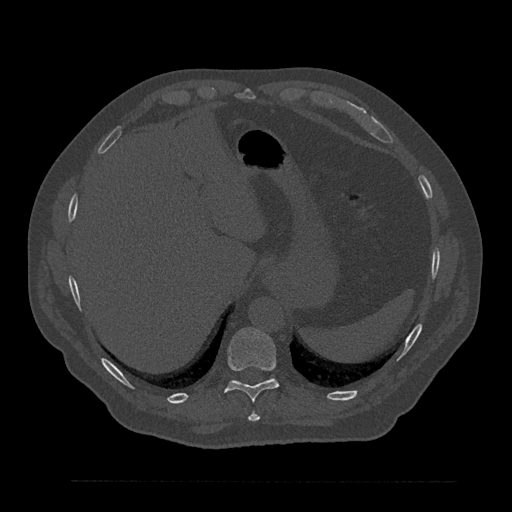
CT including the spine, one axial slice. Reconstruction kernel Br40s/3. Bone window (W 1800 / L 400 HU). 0.5 mm slice thickness. 512 × 512 image matrix, field of view 430 × 430 mm. Male patient, age 61 years. Case-level facts recorded for this patient, not image findings: primary cancer: prostate.
Annotated regions visible in this slice (semi-automatically segmented with operator editing):
- T10 vertebra: bounding box [x1, y1, x2, y2] px = [225, 328, 279, 402]
- T9 vertebra: [248, 412, 260, 422]